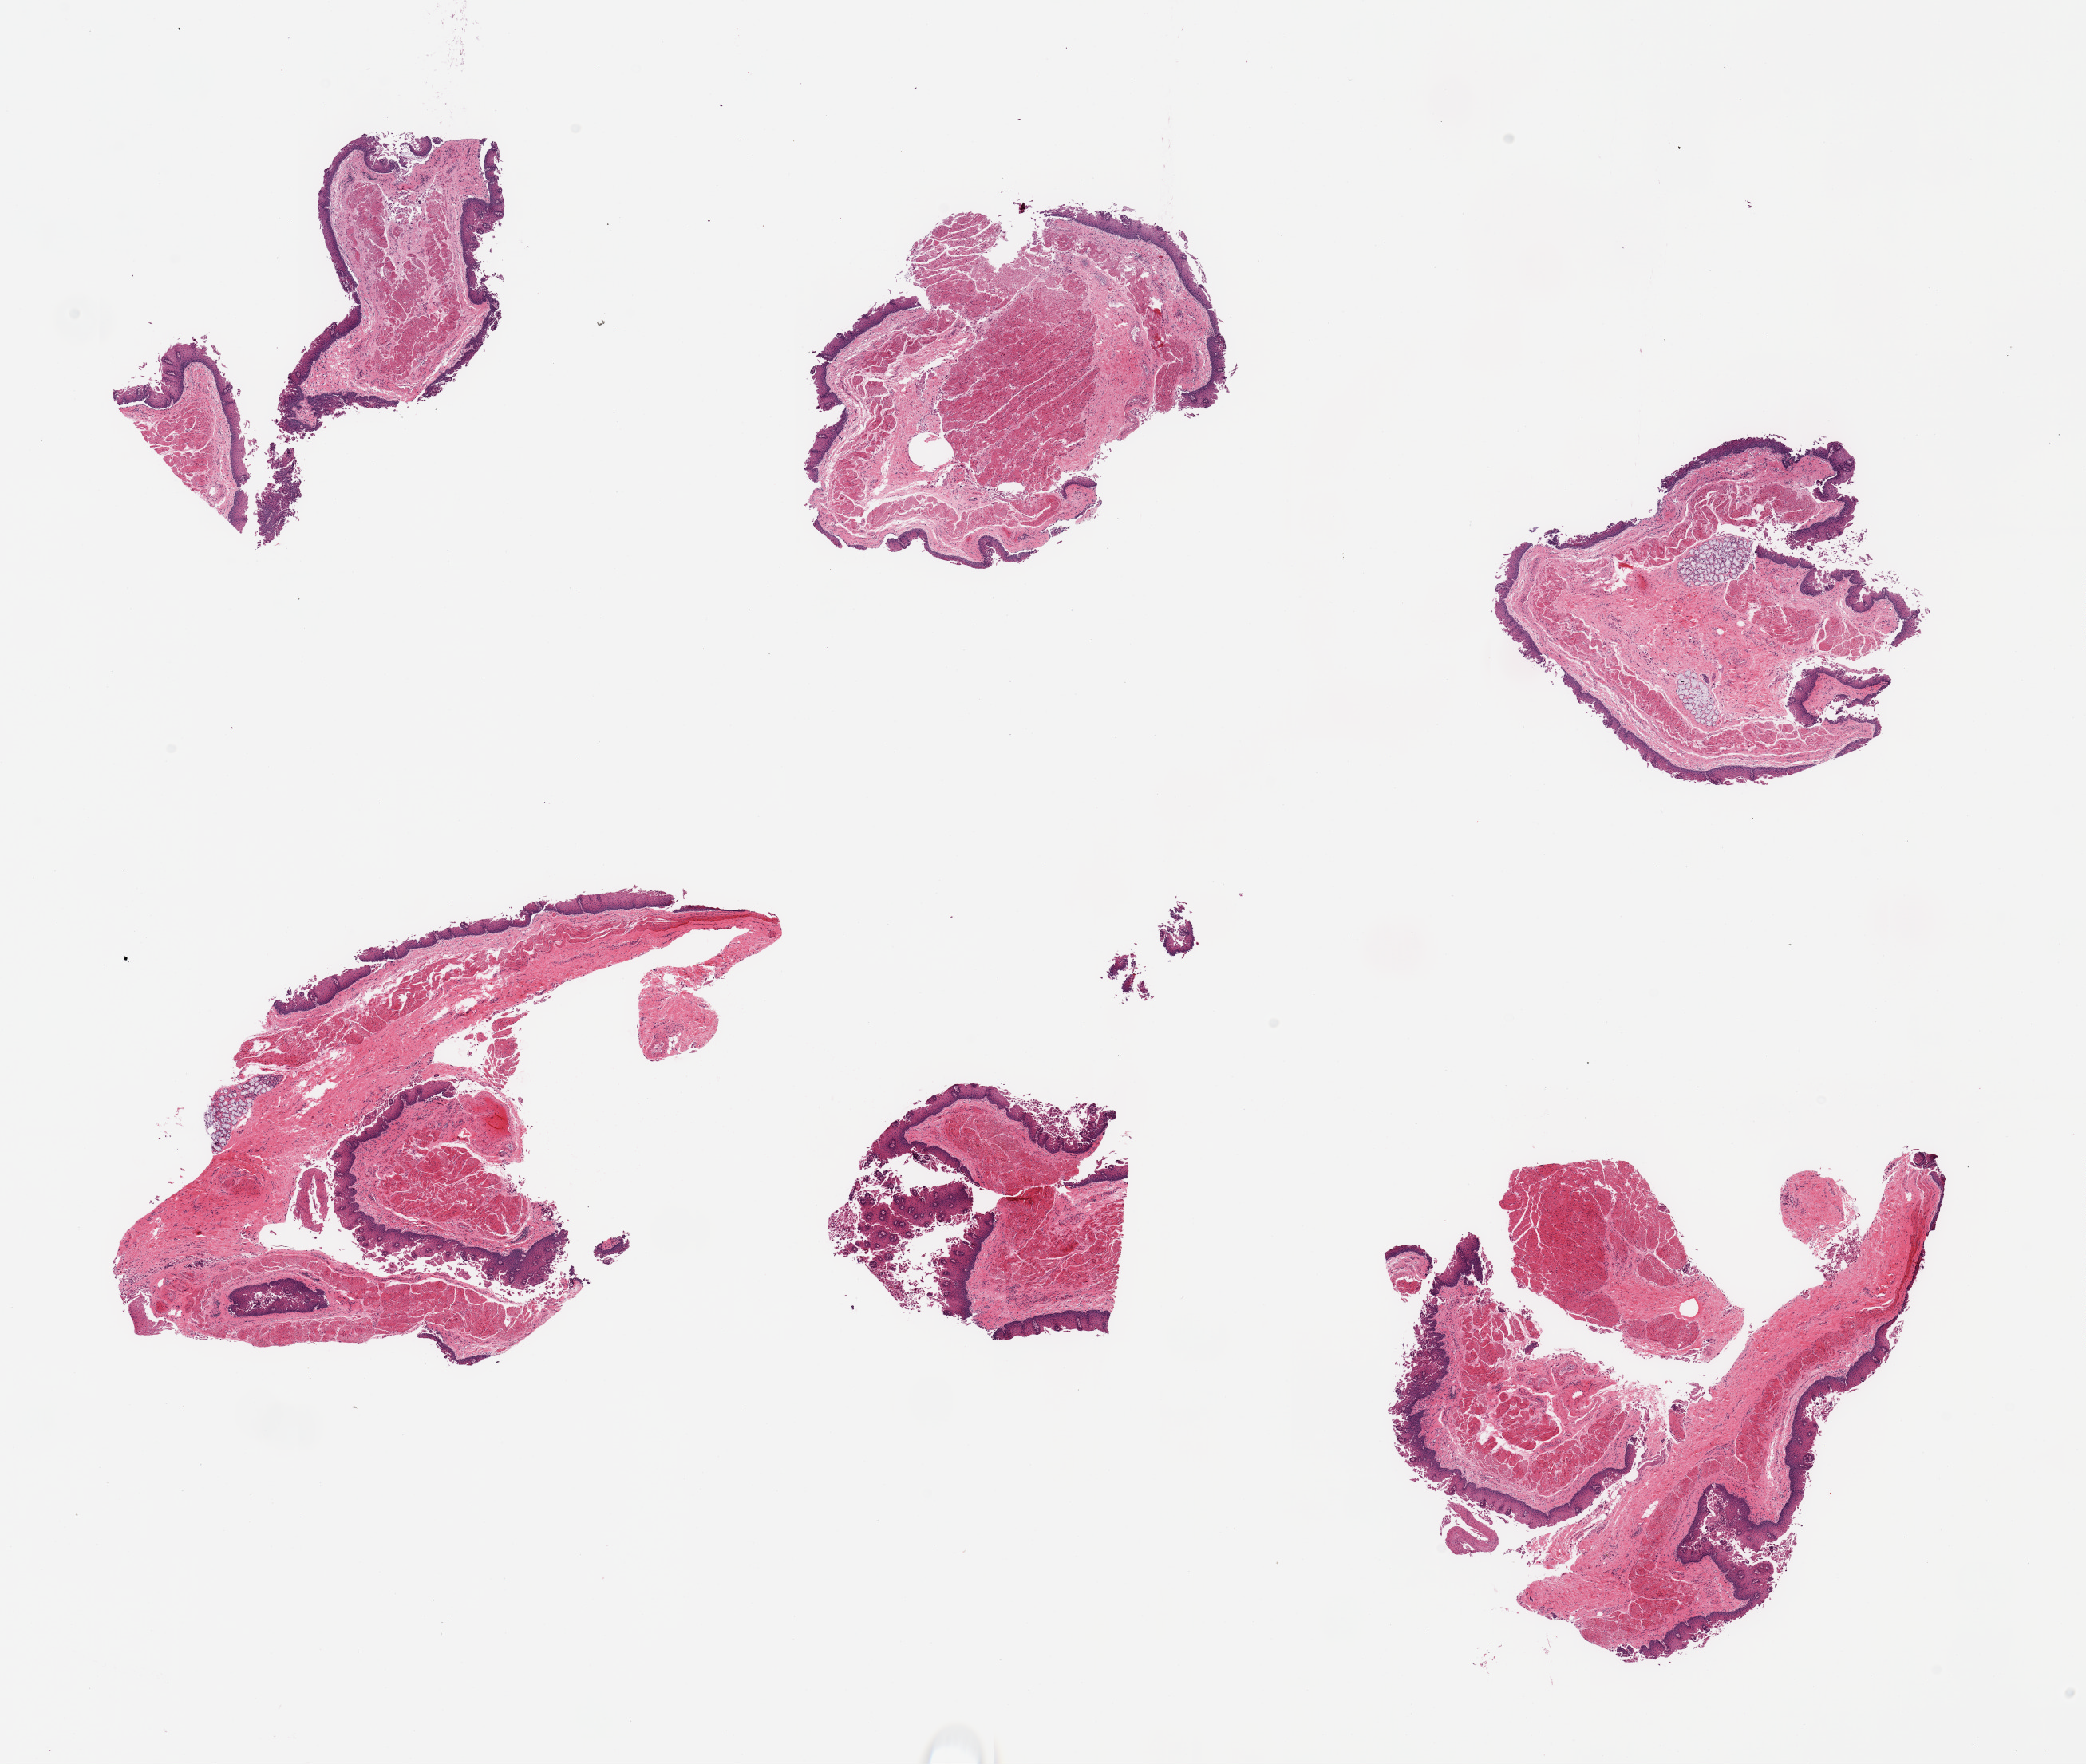
Hematoxylin and eosin (H&E) whole-slide image — a low-resolution overview of the entire scanned area, about 20.7 x 17.5 mm (slide scanned at 20x); PAXgene-fixed, paraffin-embedded tissue; section of esophageal mucous membrane (target tissue); tissue donor sample. Donor sex: male.
Pathologist's review note for this sample: 6 pieces with some fragmentation; squamous epithelium with superficial desquamation; few pieces contain submucosal glands, small portion of muscularis propria.